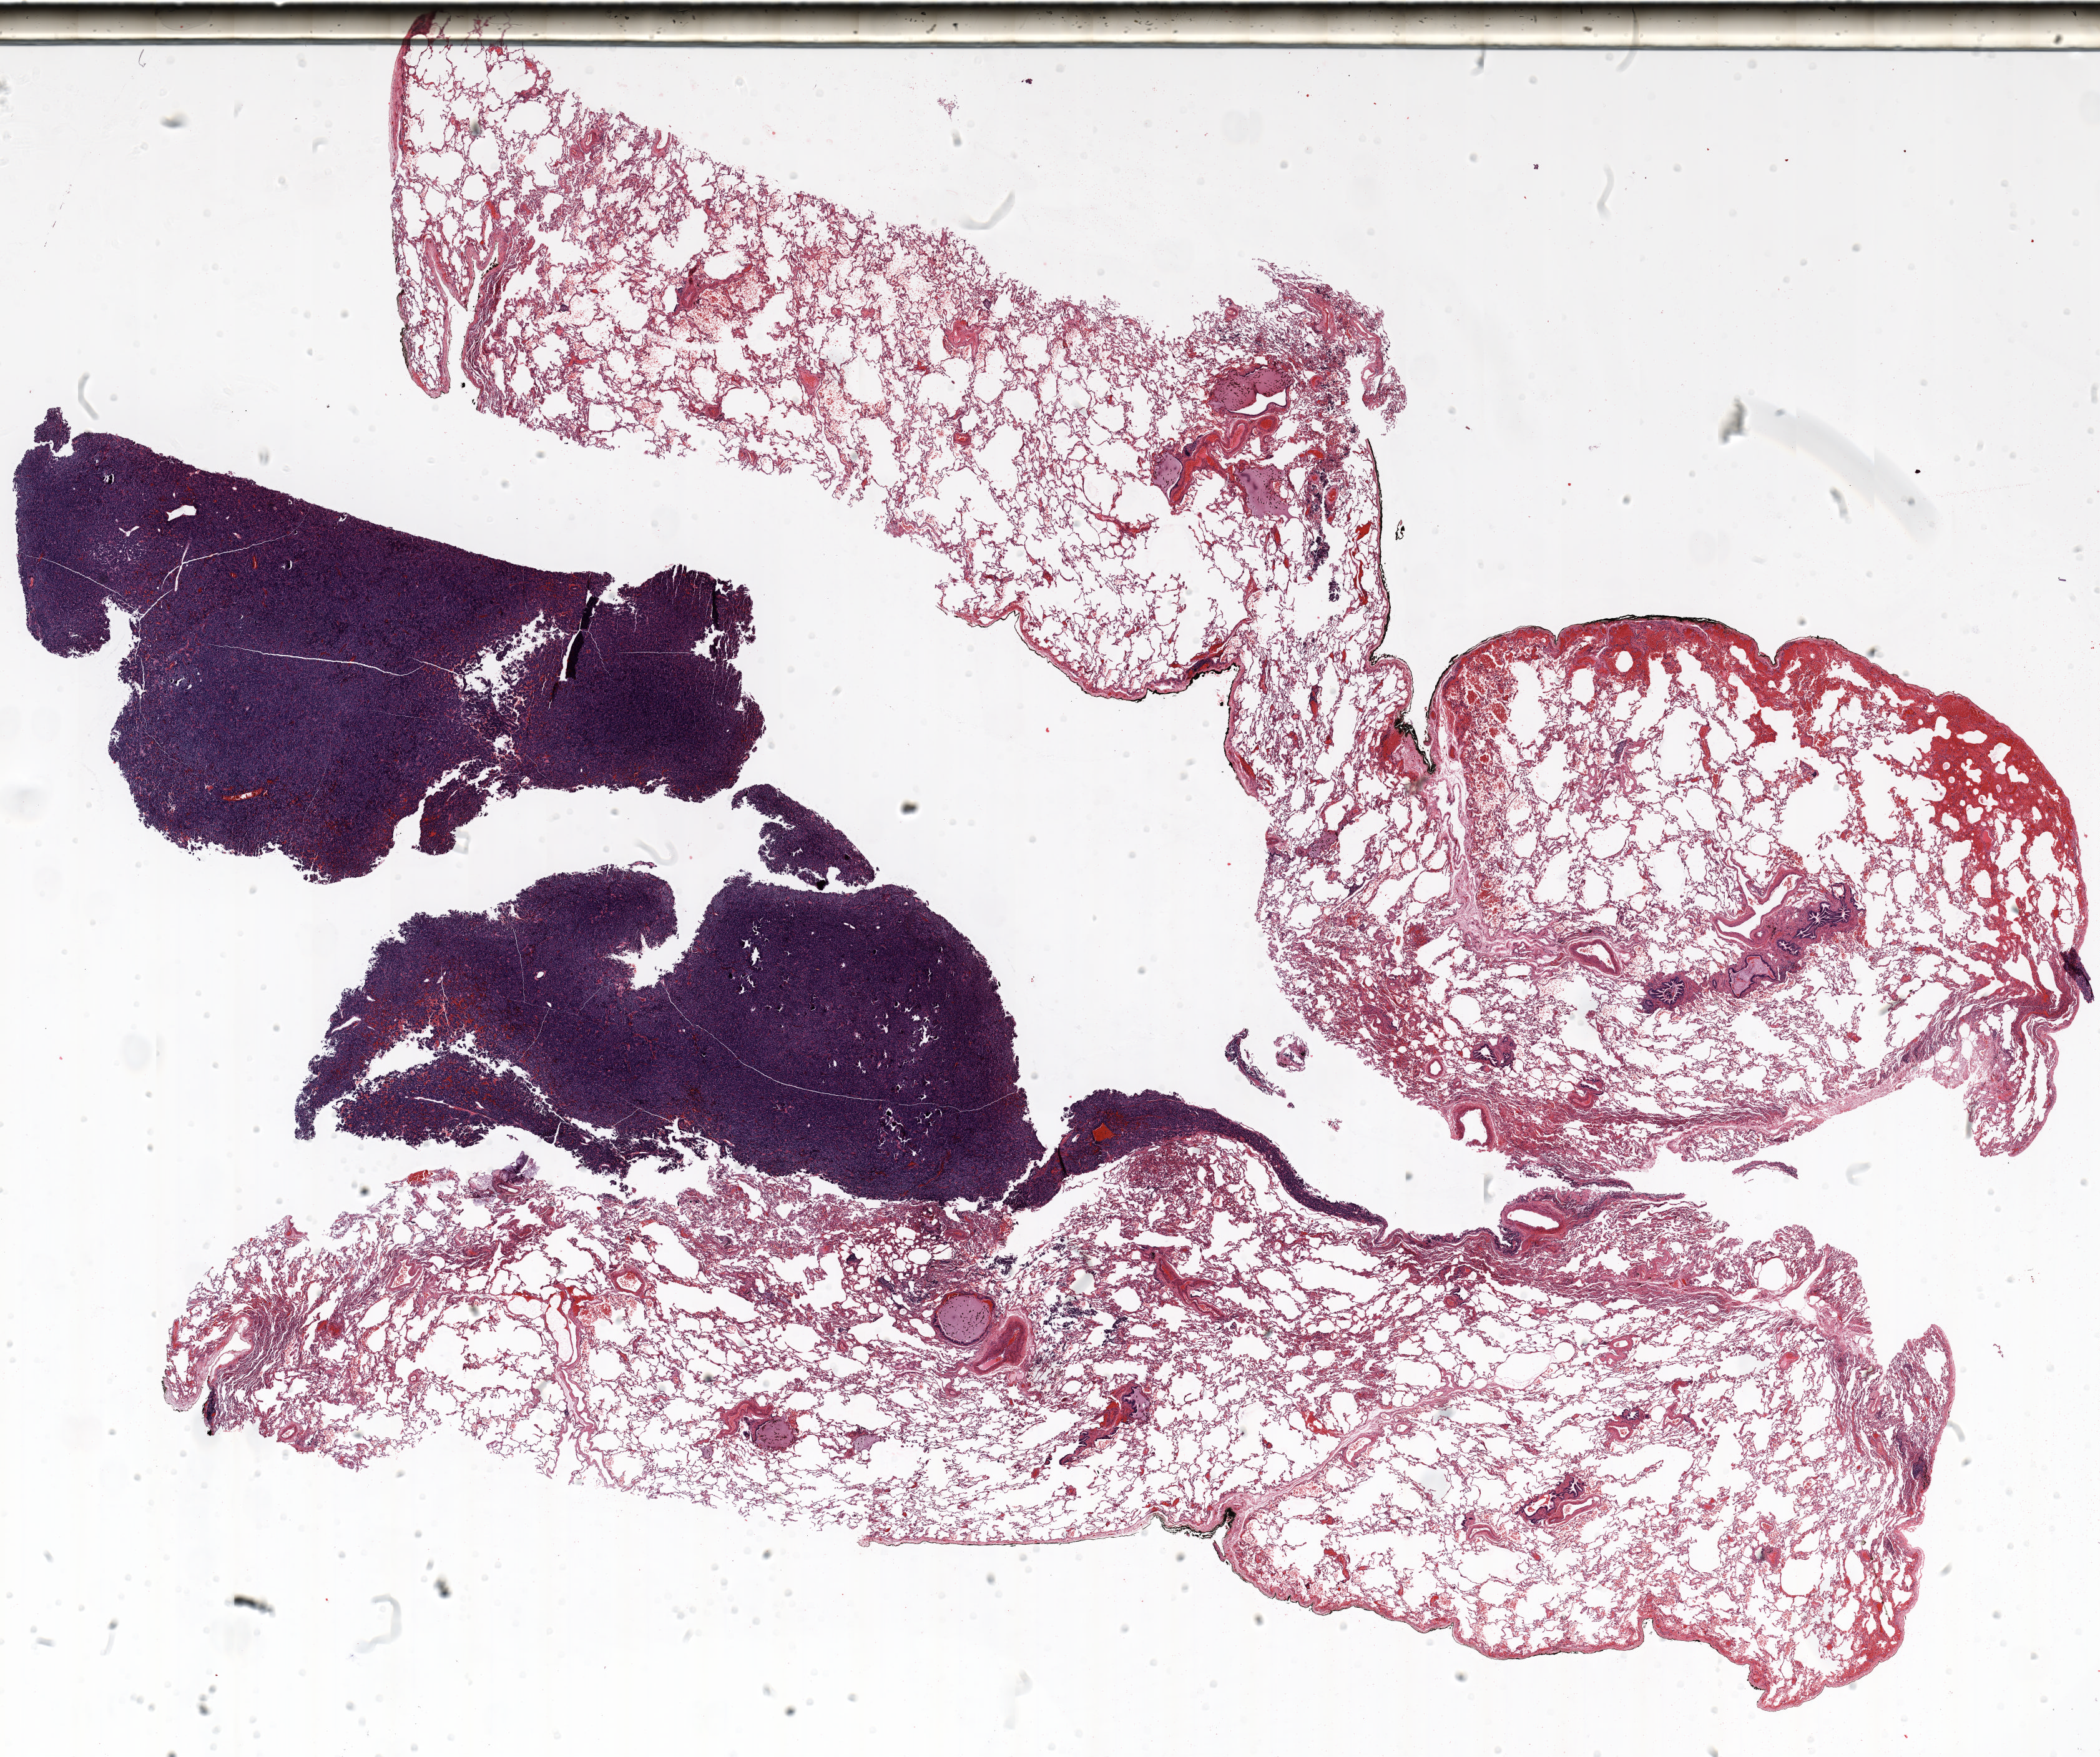
Whole-slide histology image, H&E-stained, low-resolution overview of the scanned area, about 27.0 x 22.6 mm (from a 20x scan). Formalin-fixed paraffin-embedded (FFPE) section. Lung. Female patient, aged 60 at enrolment.
Primary tumour location (clinical record): left lower lobe. Tumour size (pathology): 13 mm. Participant's lung-cancer diagnosis: Carcinoid tumor, NOS. Stage (AJCC 6th edition): carcinoid, stage not assessed.